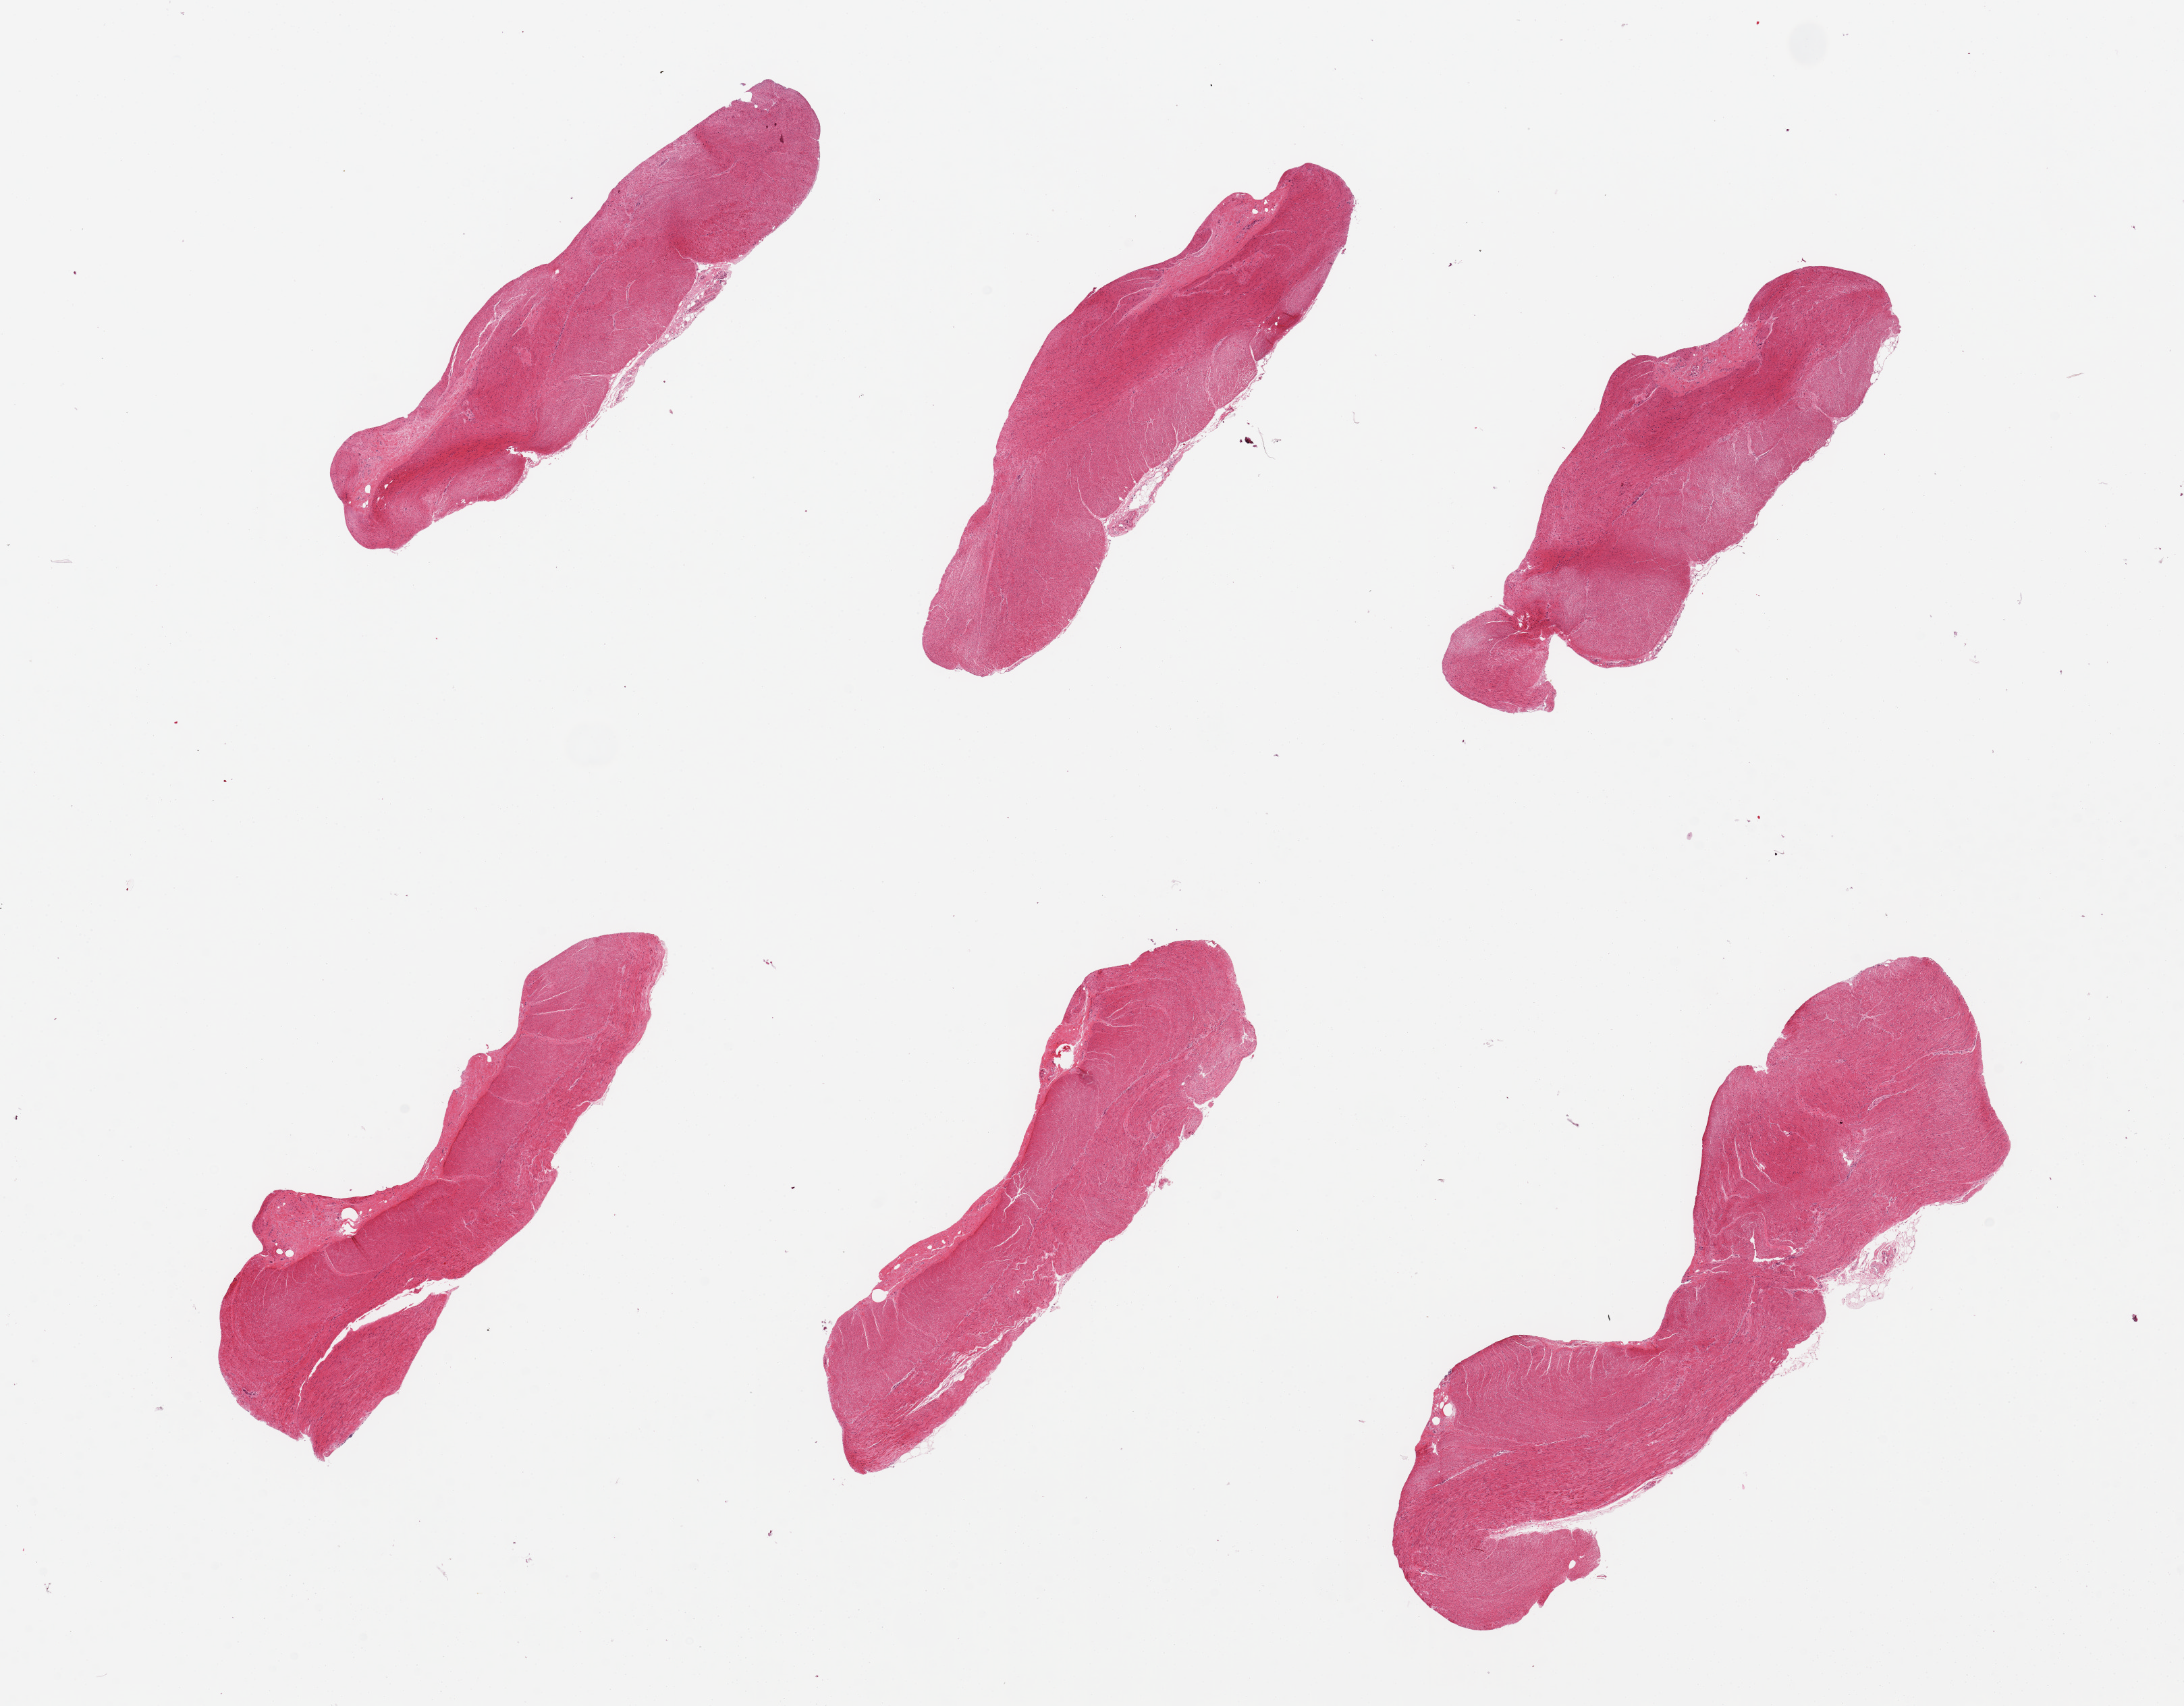
Digitized haematoxylin and eosin-stained section, a low-resolution overview of the entire scanned area, about 25.6 x 20.0 mm, PAXgene-fixed paraffin-embedded (PFPE) section, sampled site (target tissue): sigmoid colon, donor tissue sample. Donor: female.
Review note (as recorded): 6 pieces all muscularis but moderately-severely autolyzed.